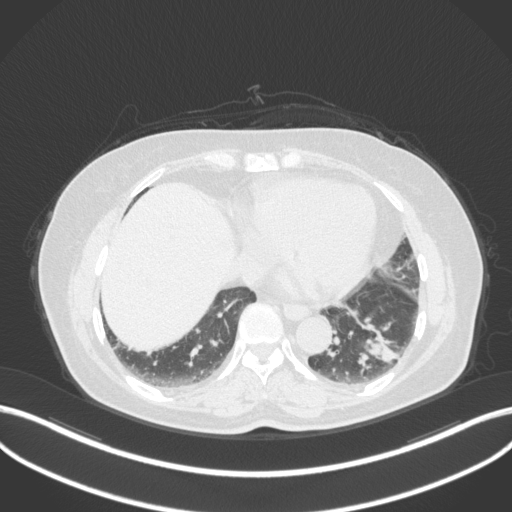
Chest CT, one axial slice; position 120 of 307 along the scan axis; reconstruction kernel B31f; lung window (W 1500 / L -600 HU); 1 mm slice thickness; 512 × 512 image matrix, field of view 400 × 400 mm. Female patient, age 59 years. Case-level facts recorded for this patient, not image findings: clinical TNM (as recorded): T2a N0 M0.
Outlined on this slice (rectangle marked by the reading radiologist):
- lung tumour (recorded histology: adenocarcinoma): bounding box [x1, y1, x2, y2] px = [350, 313, 405, 371]